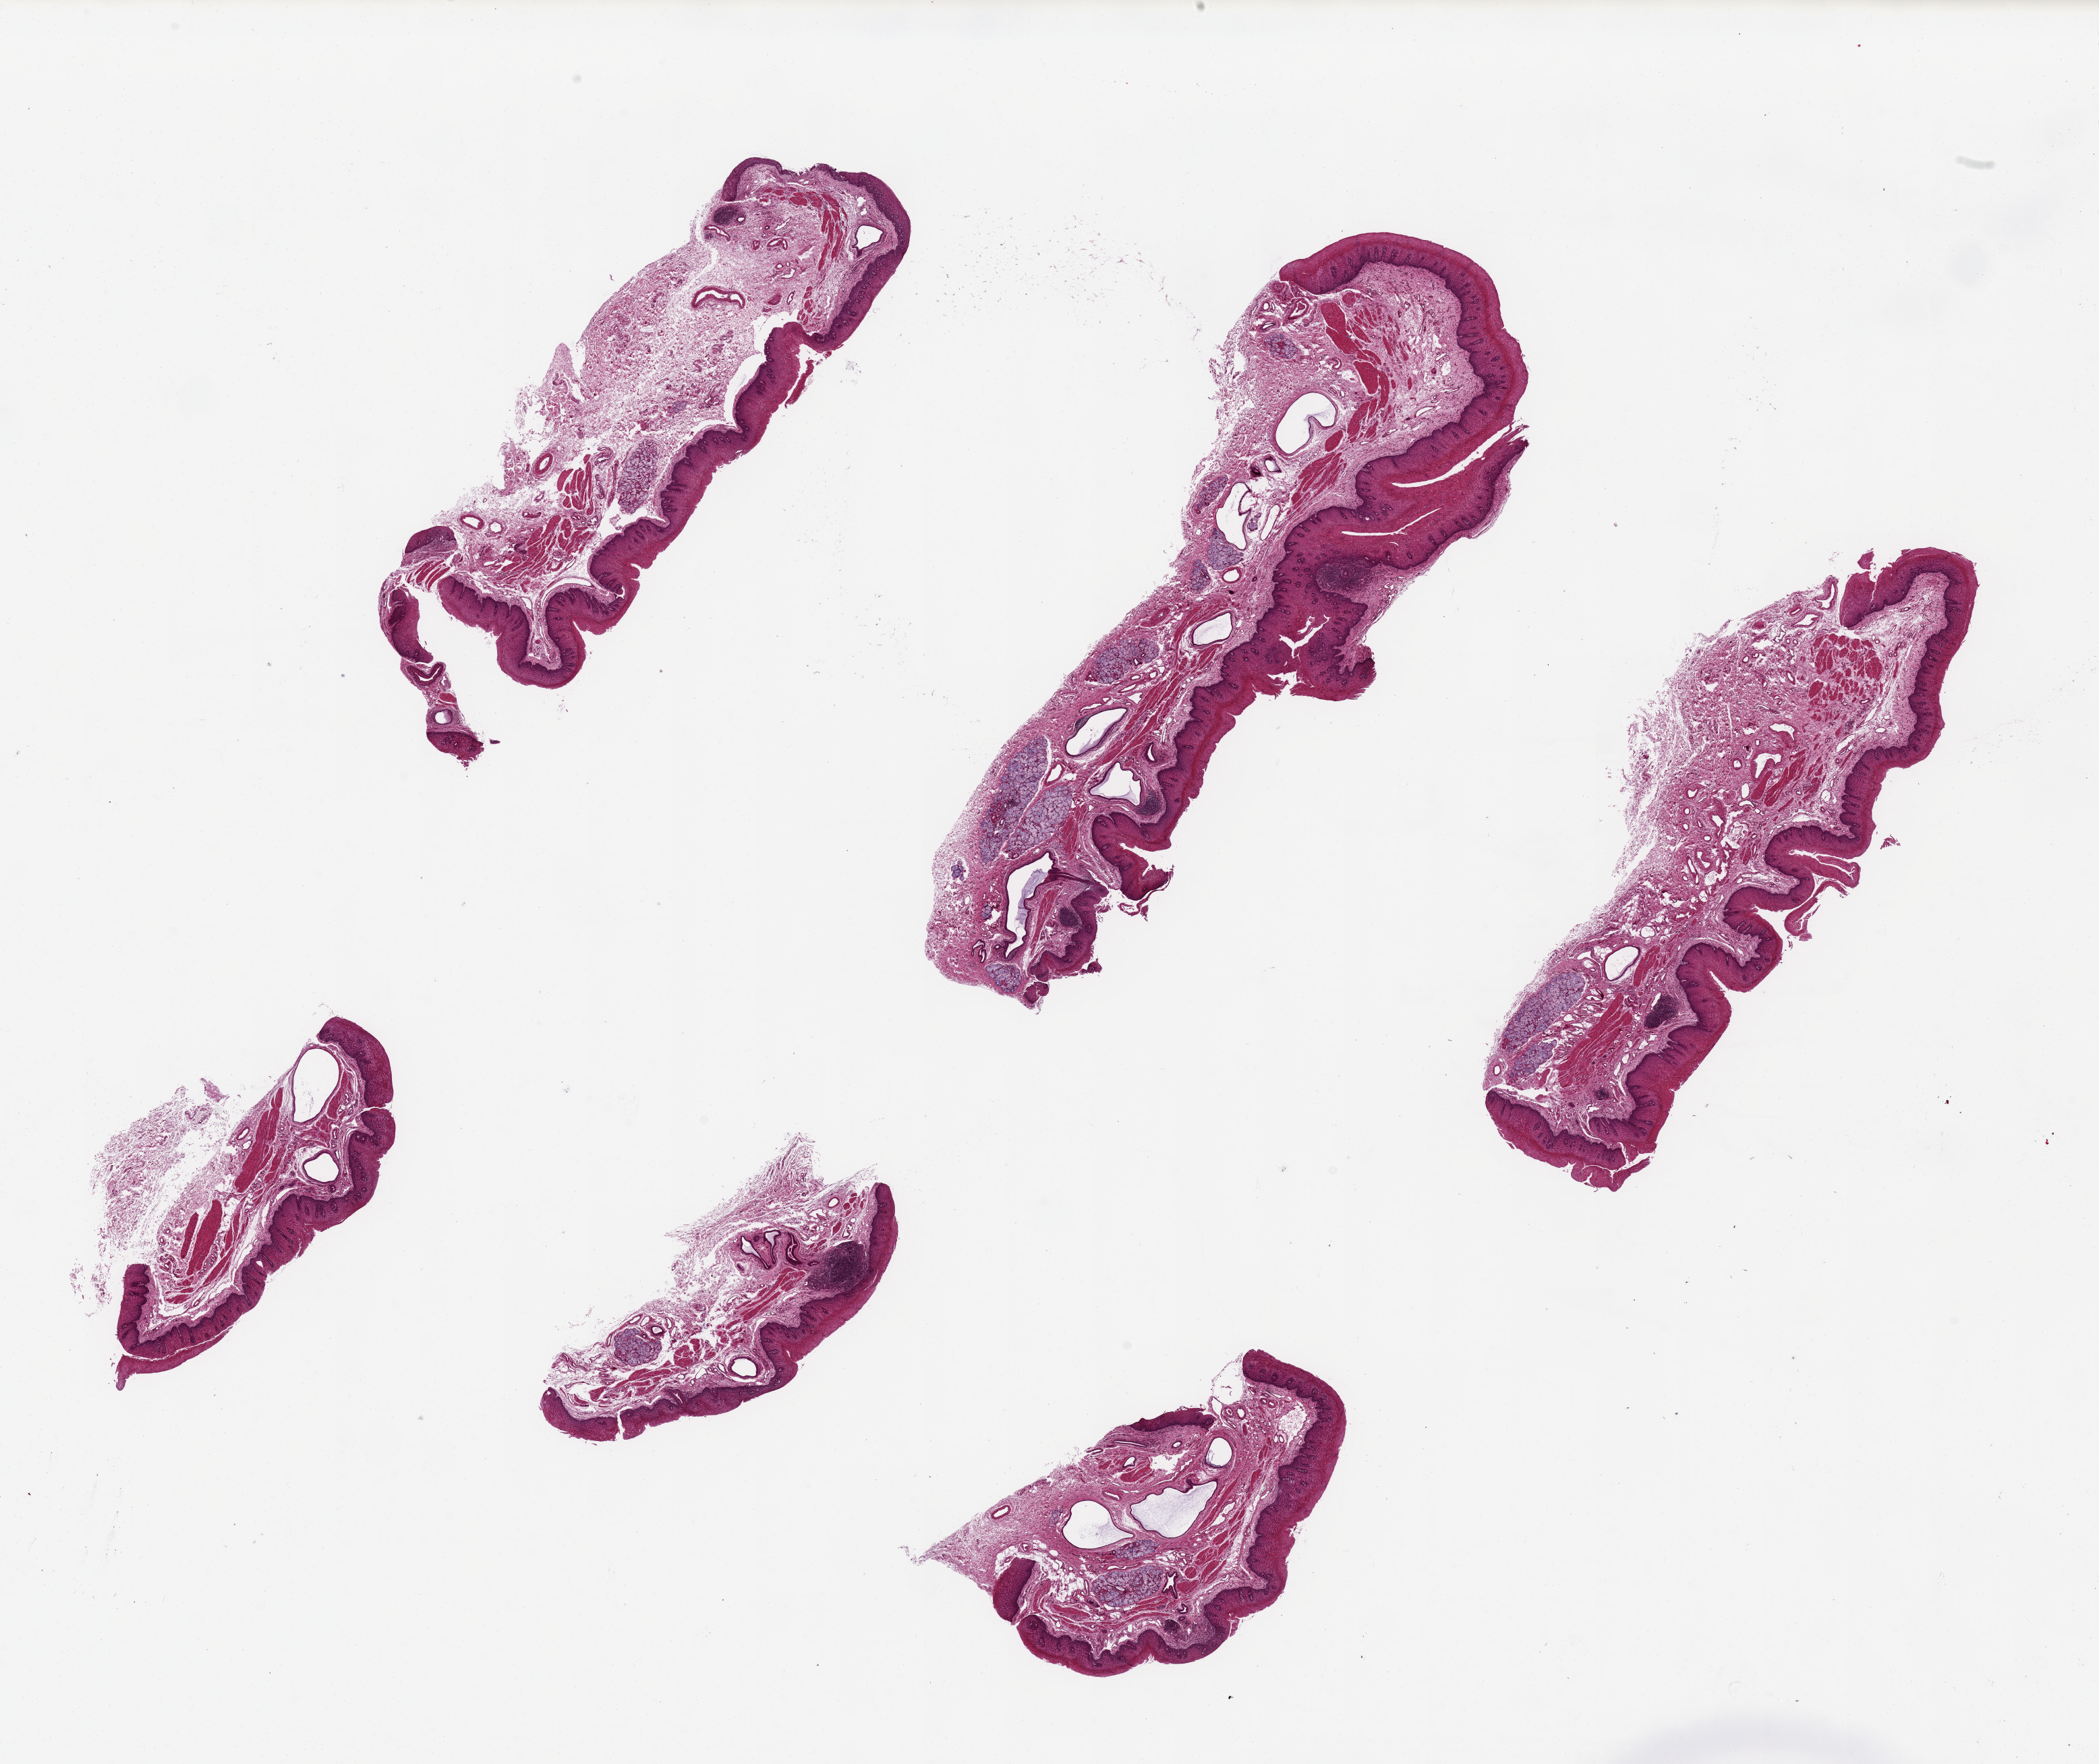
Whole-slide image, haematoxylin and eosin stain — whole scanned area (about 24.6 x 20.7 mm, slide scanned at 20x) shown as a low-resolution overview; PAXgene-fixed paraffin-embedded (PFPE) section; sampled site (target tissue): esophageal mucous membrane; donor tissue sample. Donor sex: male.
Review note (as recorded): 6 ~7x2mm pieces with squamous mucosa ~10% of thickness.